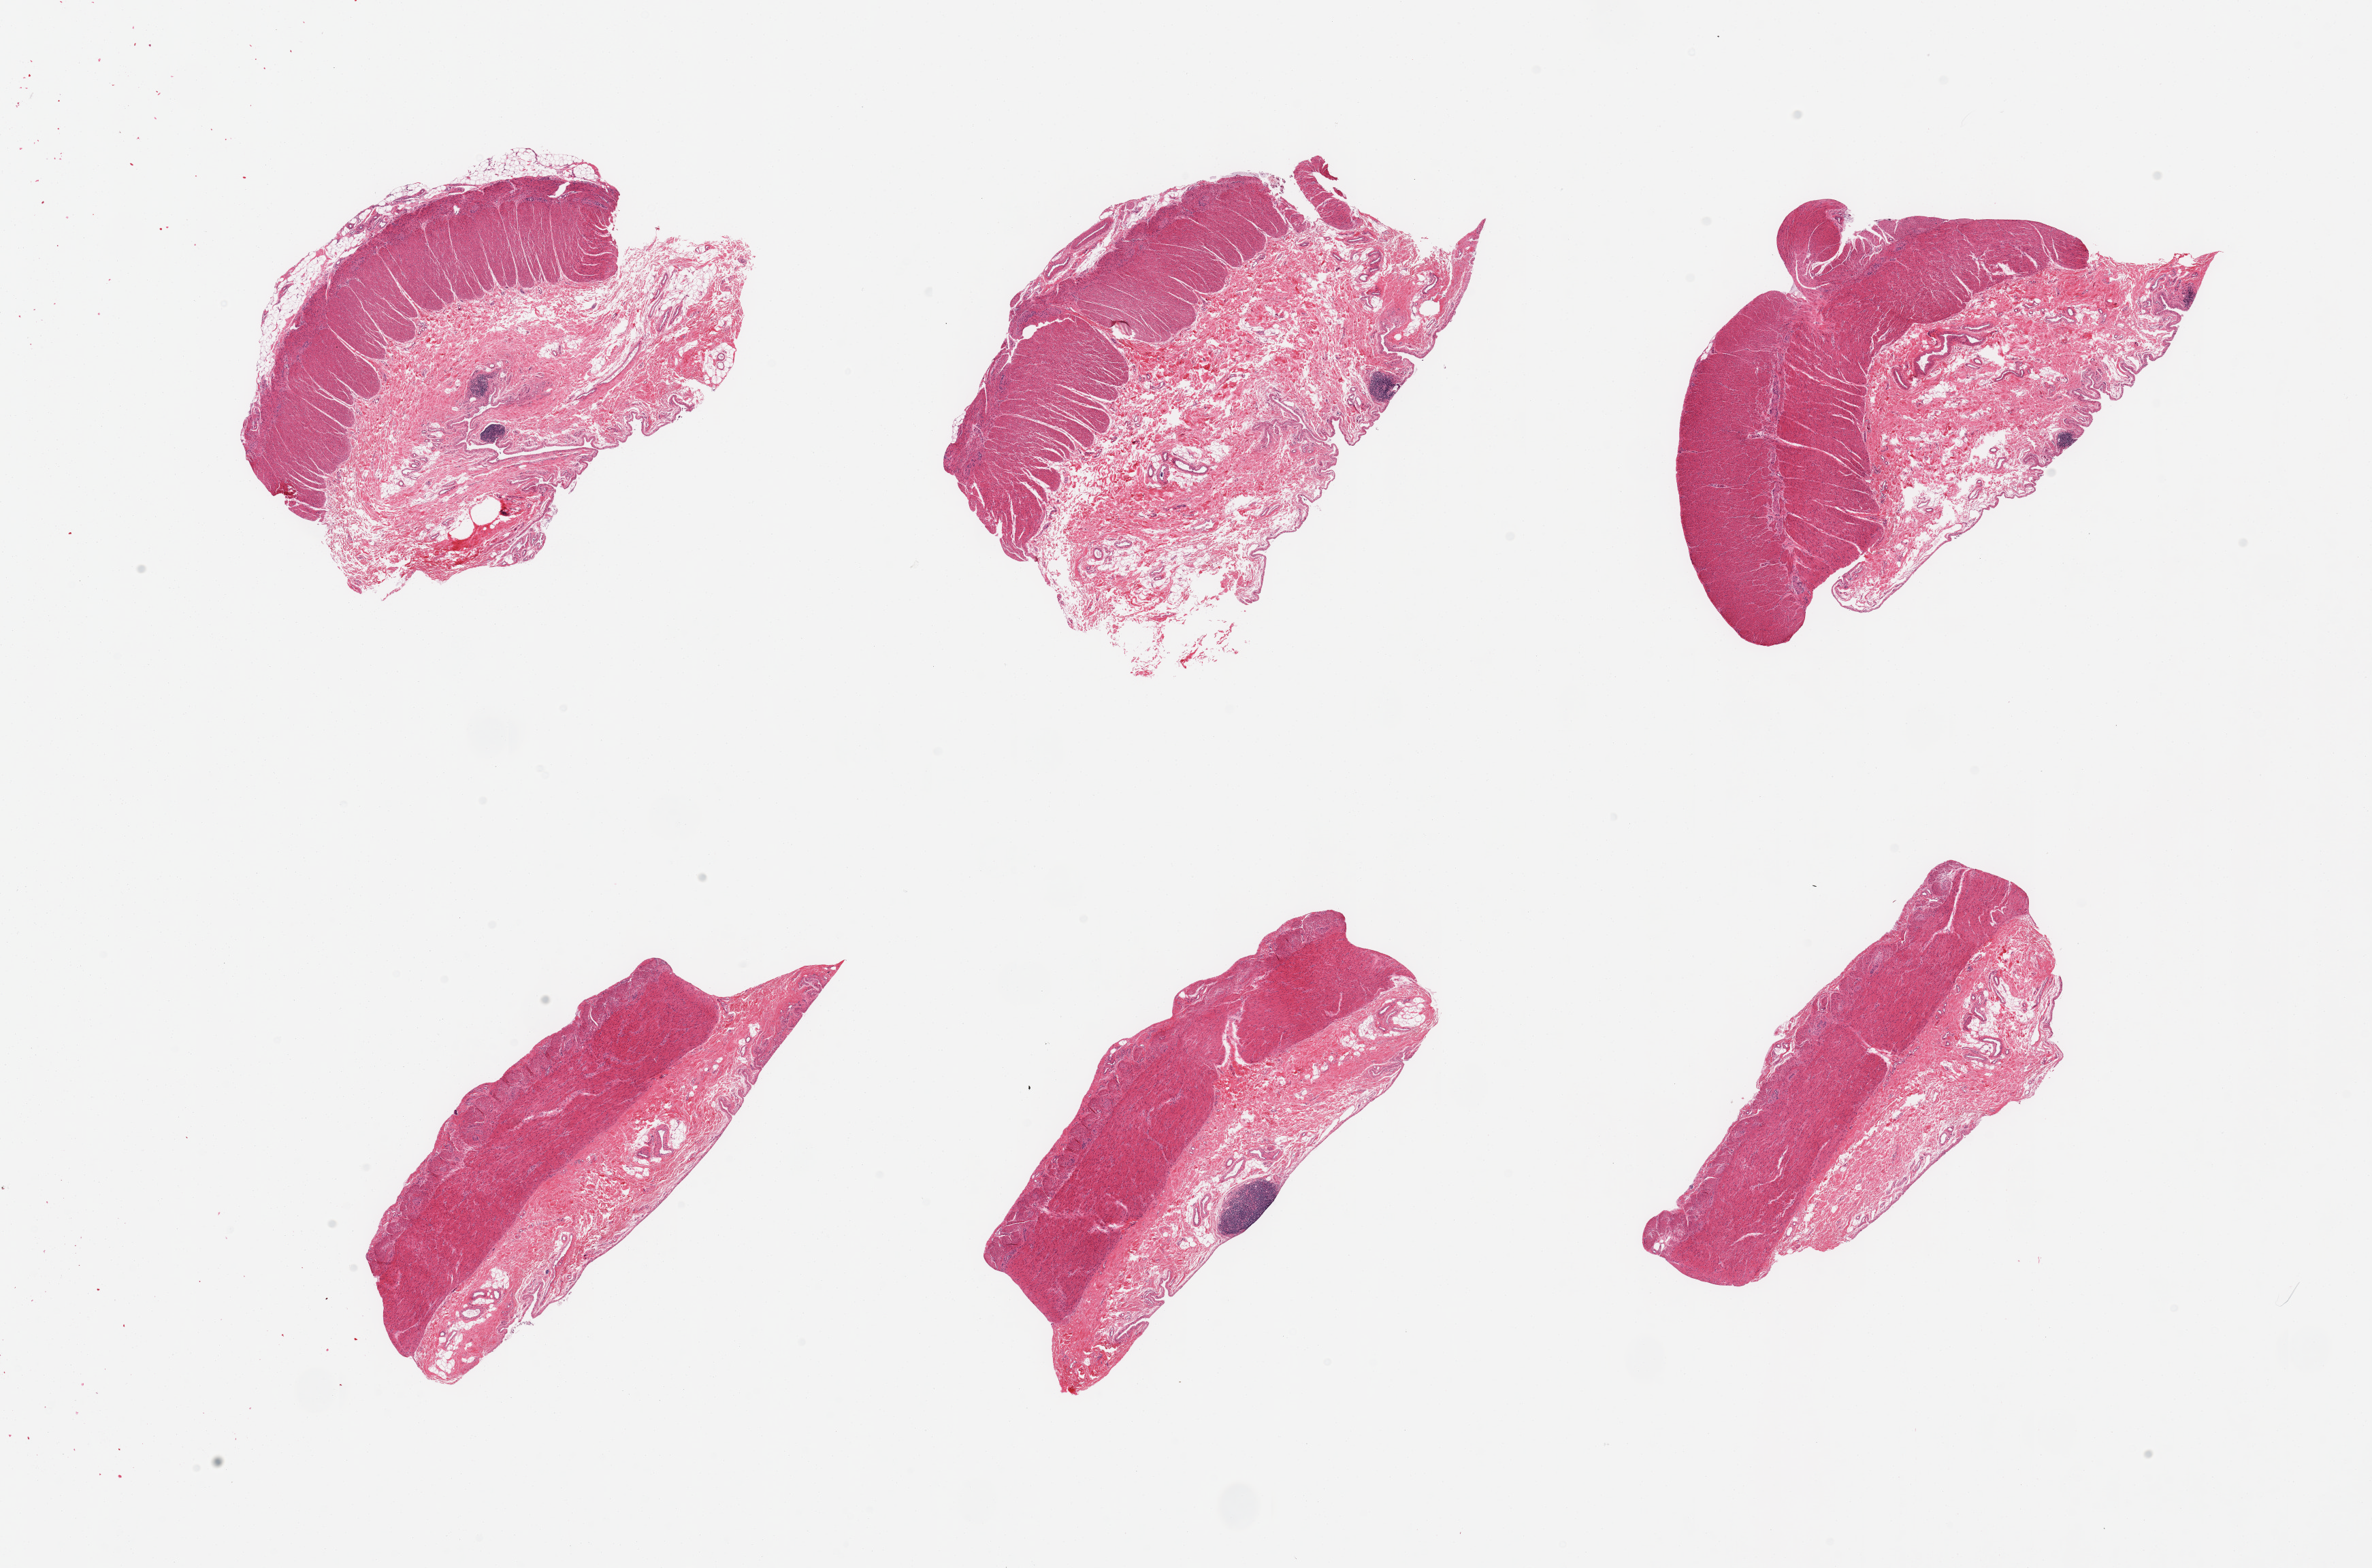
Whole-slide image, hematoxylin and eosin (H&E) stain, brightfield — low-resolution overview of the scanned area, about 27.6 x 18.2 mm. PAXgene-fixed, paraffin-embedded tissue. Section of sigmoid colon (target tissue). Tissue donor sample. Donor sex: male.
- pathologist's review note for this sample: 6 pieces, target muscularis, good specimens, incdidental lymph nodes